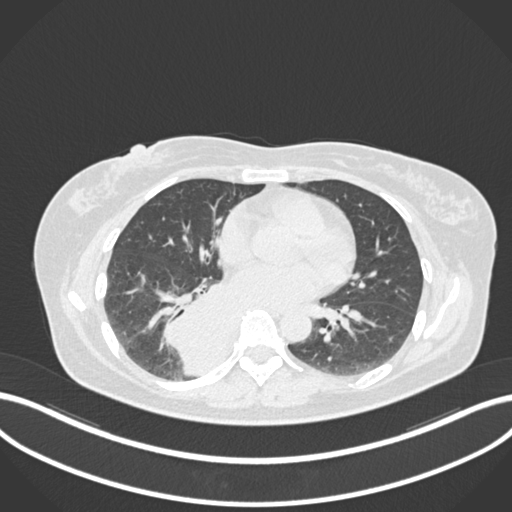
Chest CT, one axial slice. Position 575 of 677 along the scan axis. Reconstruction kernel B30f. Lung window (W 1500 / L -600 HU). 512 × 512 image matrix, field of view 400 × 400 mm. Patient: female, 54 years. From the clinical record (not read from this slice): clinical TNM (as recorded): T4 N0 M0.
Structures marked on this image (rectangle marked by the reading radiologist):
- lung tumour (recorded histology: adenocarcinoma): bounding box [x1, y1, x2, y2] px = [156, 277, 244, 379]